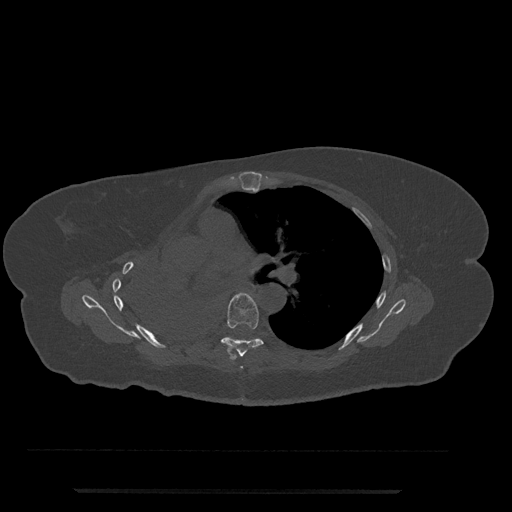
CT including the spine, one axial slice; reconstruction kernel Br40s/3; 120 kVp; bone window (W 1800 / L 400 HU); 0.5 mm slice thickness; 512 × 512 image matrix. Female patient, age 51 years. From the clinical record (not read from this slice): primary cancer: neuro; vertebrae with lytic lesions (as recorded): T8.
Outlined on this slice (semi-automatically segmented with operator editing):
- T5 vertebra: bounding box <240,366,243,369> (left, top, right, bottom; pixels)
- T6 vertebra: <221,293,263,359>
- T7 vertebra: <227,337,231,339>